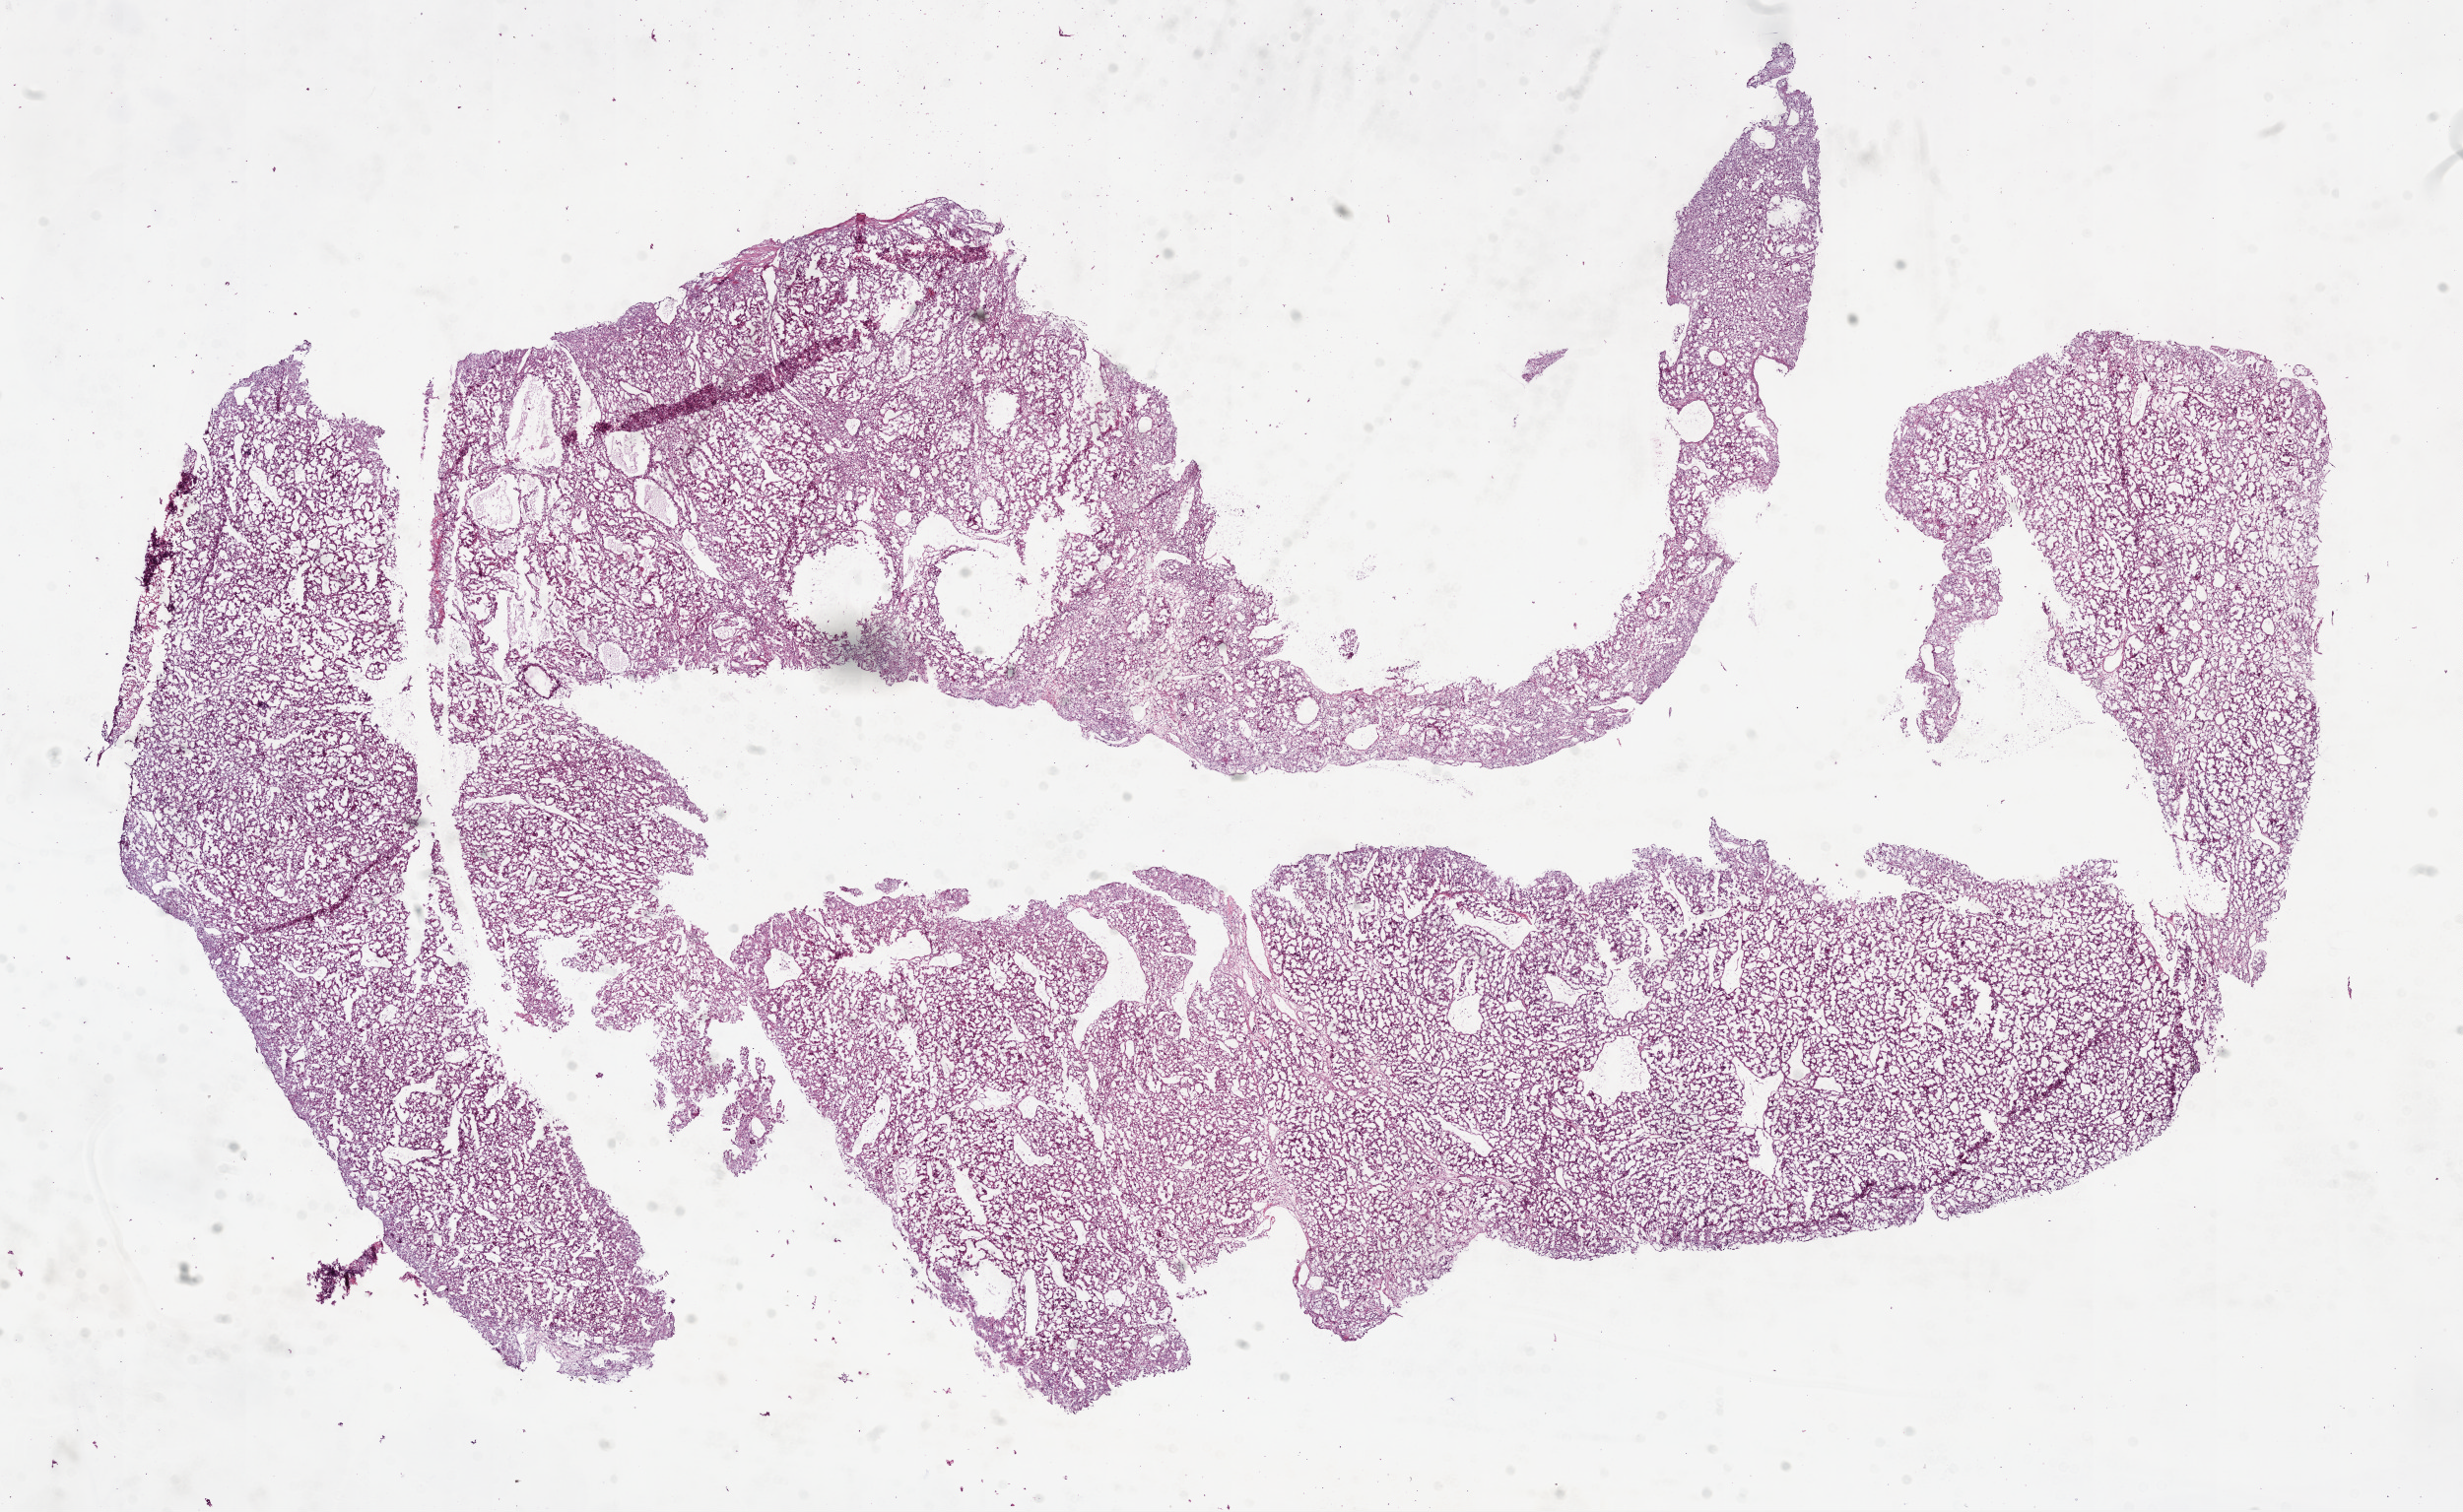
H&E-stained whole-slide image, shown as a low-resolution overview of the whole scanned area (about 20.1 x 12.3 mm), frozen section from the bottom of the tissue portion, kidney, primary tumour sample. Male patient; age at initial diagnosis 56 years. Composition of this section per pathologist review: tumour cells 95%, tumour nuclei 90%.
Pathologic diagnosis: Clear cell adenocarcinoma, NOS.